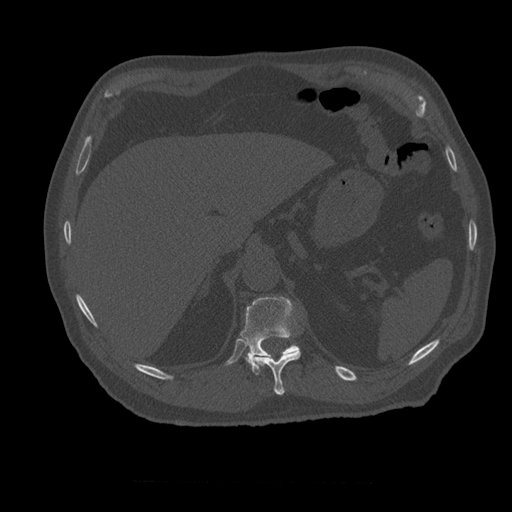
CT including the spine, one axial slice. Slice 272 of 399 in the series (ordered by position). Reconstruction kernel STANDARD. 120 kVp. Bone window (W 1800 / L 400 HU). 1.25 mm slice thickness. 512 × 512 image matrix, field of view 407 × 407 mm. Patient age 73 years. From the clinical record (not read from this slice): primary cancer: prostate.
Outlined on this slice (semi-automatically segmented with operator editing):
- T11 vertebra: bounding box (x1, y1, x2, y2) in pixels: (249, 350, 301, 396)
- T12 vertebra: (240, 297, 300, 374)